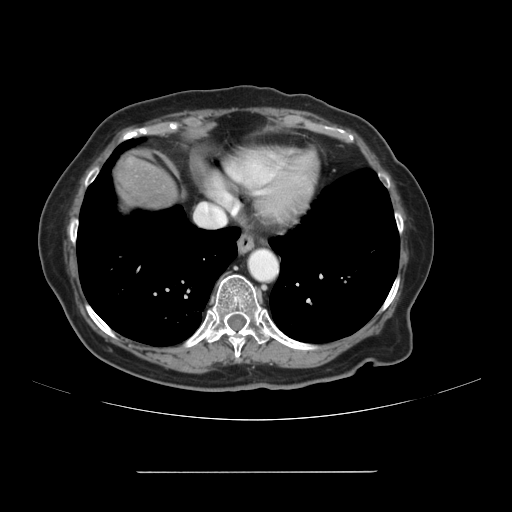
Contrast-enhanced abdominal CT, one axial slice; slice 105 of 111 in the series (ordered by position); 120 kVp; intravenous contrast given; soft-tissue window (W 400 / L 40 HU); 2.5 mm slice thickness; 512 × 512 image matrix, field of view 400 × 400 mm. Female patient, age 74 years. From the clinical record (not read from this slice): diagnosis: colorectal cancer liver metastases, imaged before liver resection; multiple liver metastases: yes; largest metastasis: 1.1 cm.
Outlined on this slice (manually delineated by an expert):
- liver: bounding box <113,155,176,212> (left, top, right, bottom; pixels)